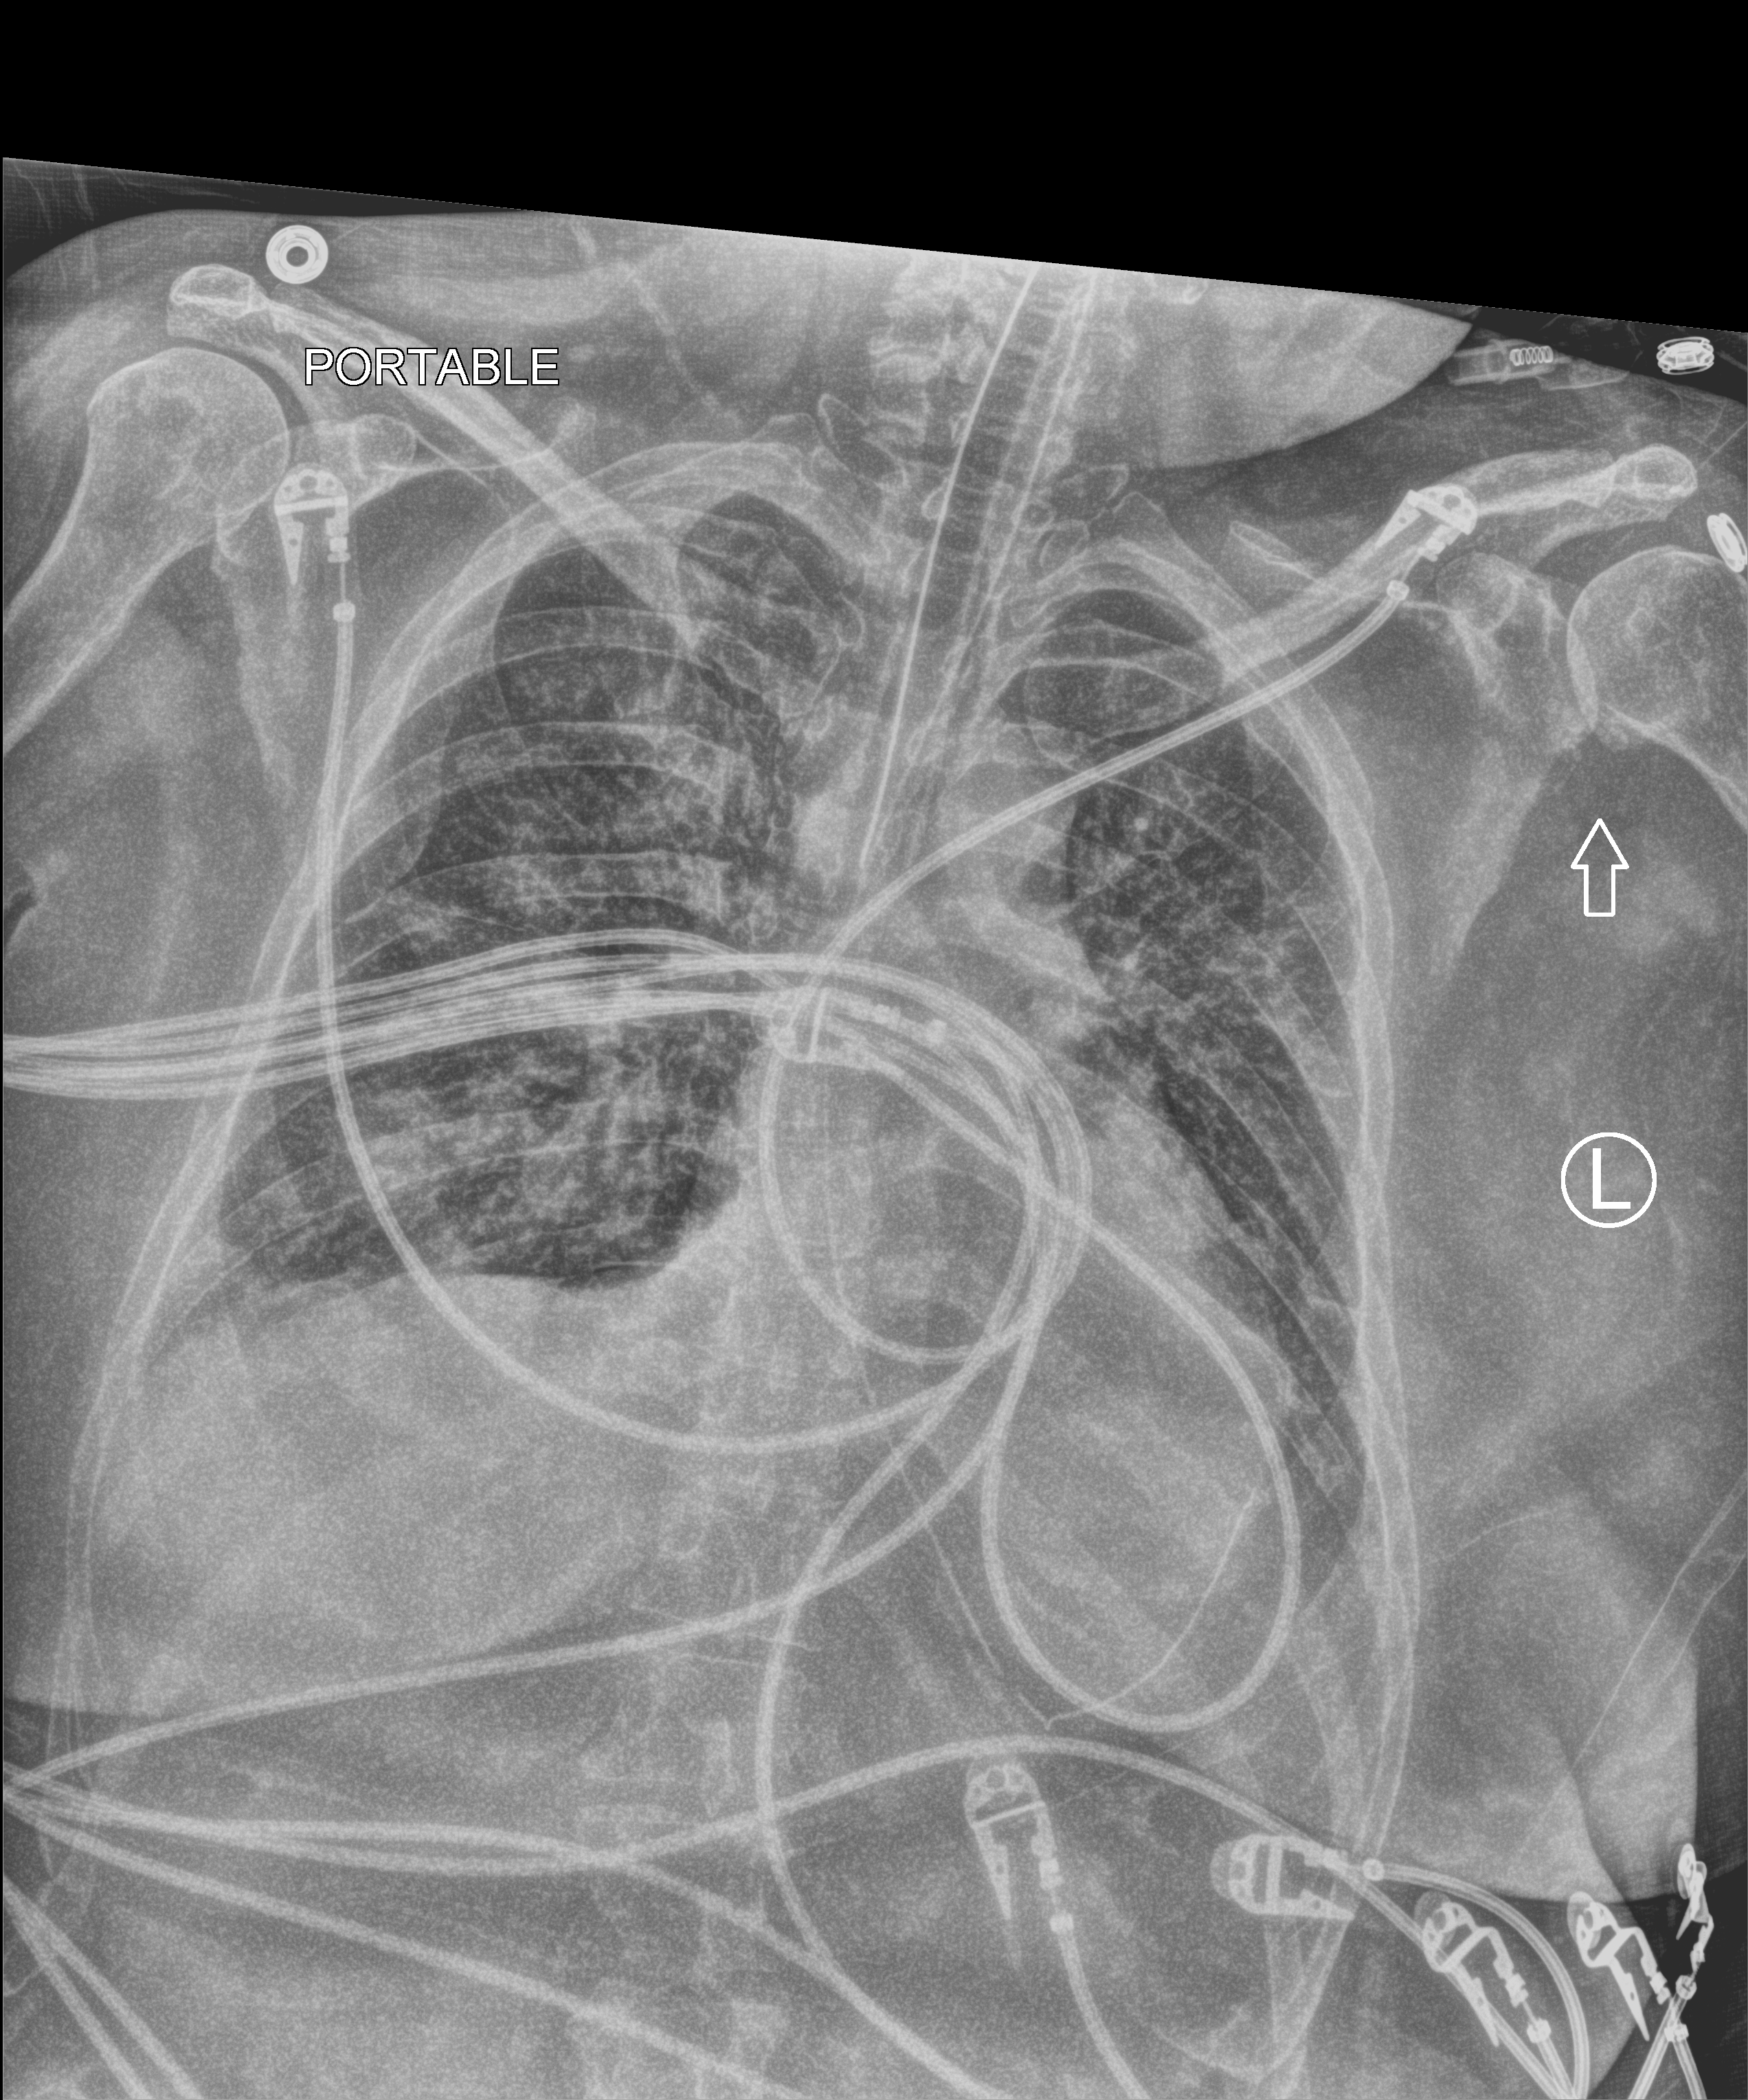
Chest X-ray (portable); anteroposterior (AP) projection. Patient hospitalised with COVID-19, aged 18–59 years.
Hospital-stay facts (about this admission, not read from this image; timing relative to this image not recorded):
- mechanically ventilated during this hospital stay: yes
- admitted to intensive care during this hospital stay: yes